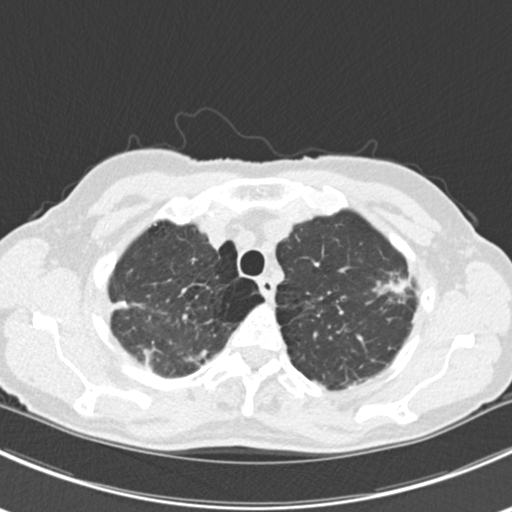
Chest CT (low-dose screening protocol), one axial image, baseline annual screen, lung window (W 1500 / L -600 HU), 512 × 512 image matrix, field of view 310 × 310 mm. Female participant, aged 63 years at enrolment.
Lesion marked by an expert reader, bounding box [x1, y1, x2, y2] px = [366, 259, 423, 317]. The screening reader recorded 10 non-calcified nodules or masses ≥4 mm on this exam (right lower lobe, right lower lobe, left lower lobe, left lower lobe, right middle lobe, right lower lobe, left lower lobe, left upper lobe, right upper lobe, left upper lobe); which of them this box marks is not recorded. Official screen result: positive, change unspecified: nodule(s) >= 4 mm or enlarging nodule(s), mass(es), or other non-specific abnormalities suspicious for lung cancer. Lung cancer was diagnosed 751 days after this screen: bronchiolo-alveolar adenocarcinoma, NOS, right upper lobe, right middle lobe, right lower lobe, left upper lobe, left lower lobe, moderately differentiated (G2), stage IV (AJCC 6th edition).